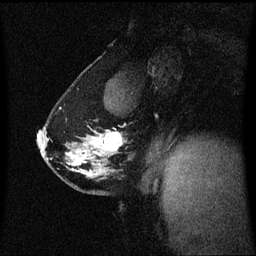
Breast MRI (dynamic contrast-enhanced), one sagittal slice. Position 39 of 60 along the scan axis. Dynamic contrast-enhanced series, image 2 of 3 at this slice position (ordered by acquisition). 1.5 T. TE 4.2 ms, TR 8.4 ms. 2 mm slice thickness. 256 × 256 image matrix, field of view 210 × 210 mm. Patient: female, 40 years. From the clinical record (not read from this slice): setting: breast cancer imaged before/during neoadjuvant chemotherapy; receptor status: triple-negative.
Outlined on this slice (semi-automatically segmented with operator editing):
- analysis volume of interest (the breast-tissue region the enhancement analysis was run in; not a lesion): box from (x=38, y=125) to (x=126, y=185) px
- tumour enhancement mask (voxels above the 70 % enhancement threshold inside the analysis volume of interest): (x=38, y=133)–(x=123, y=162)